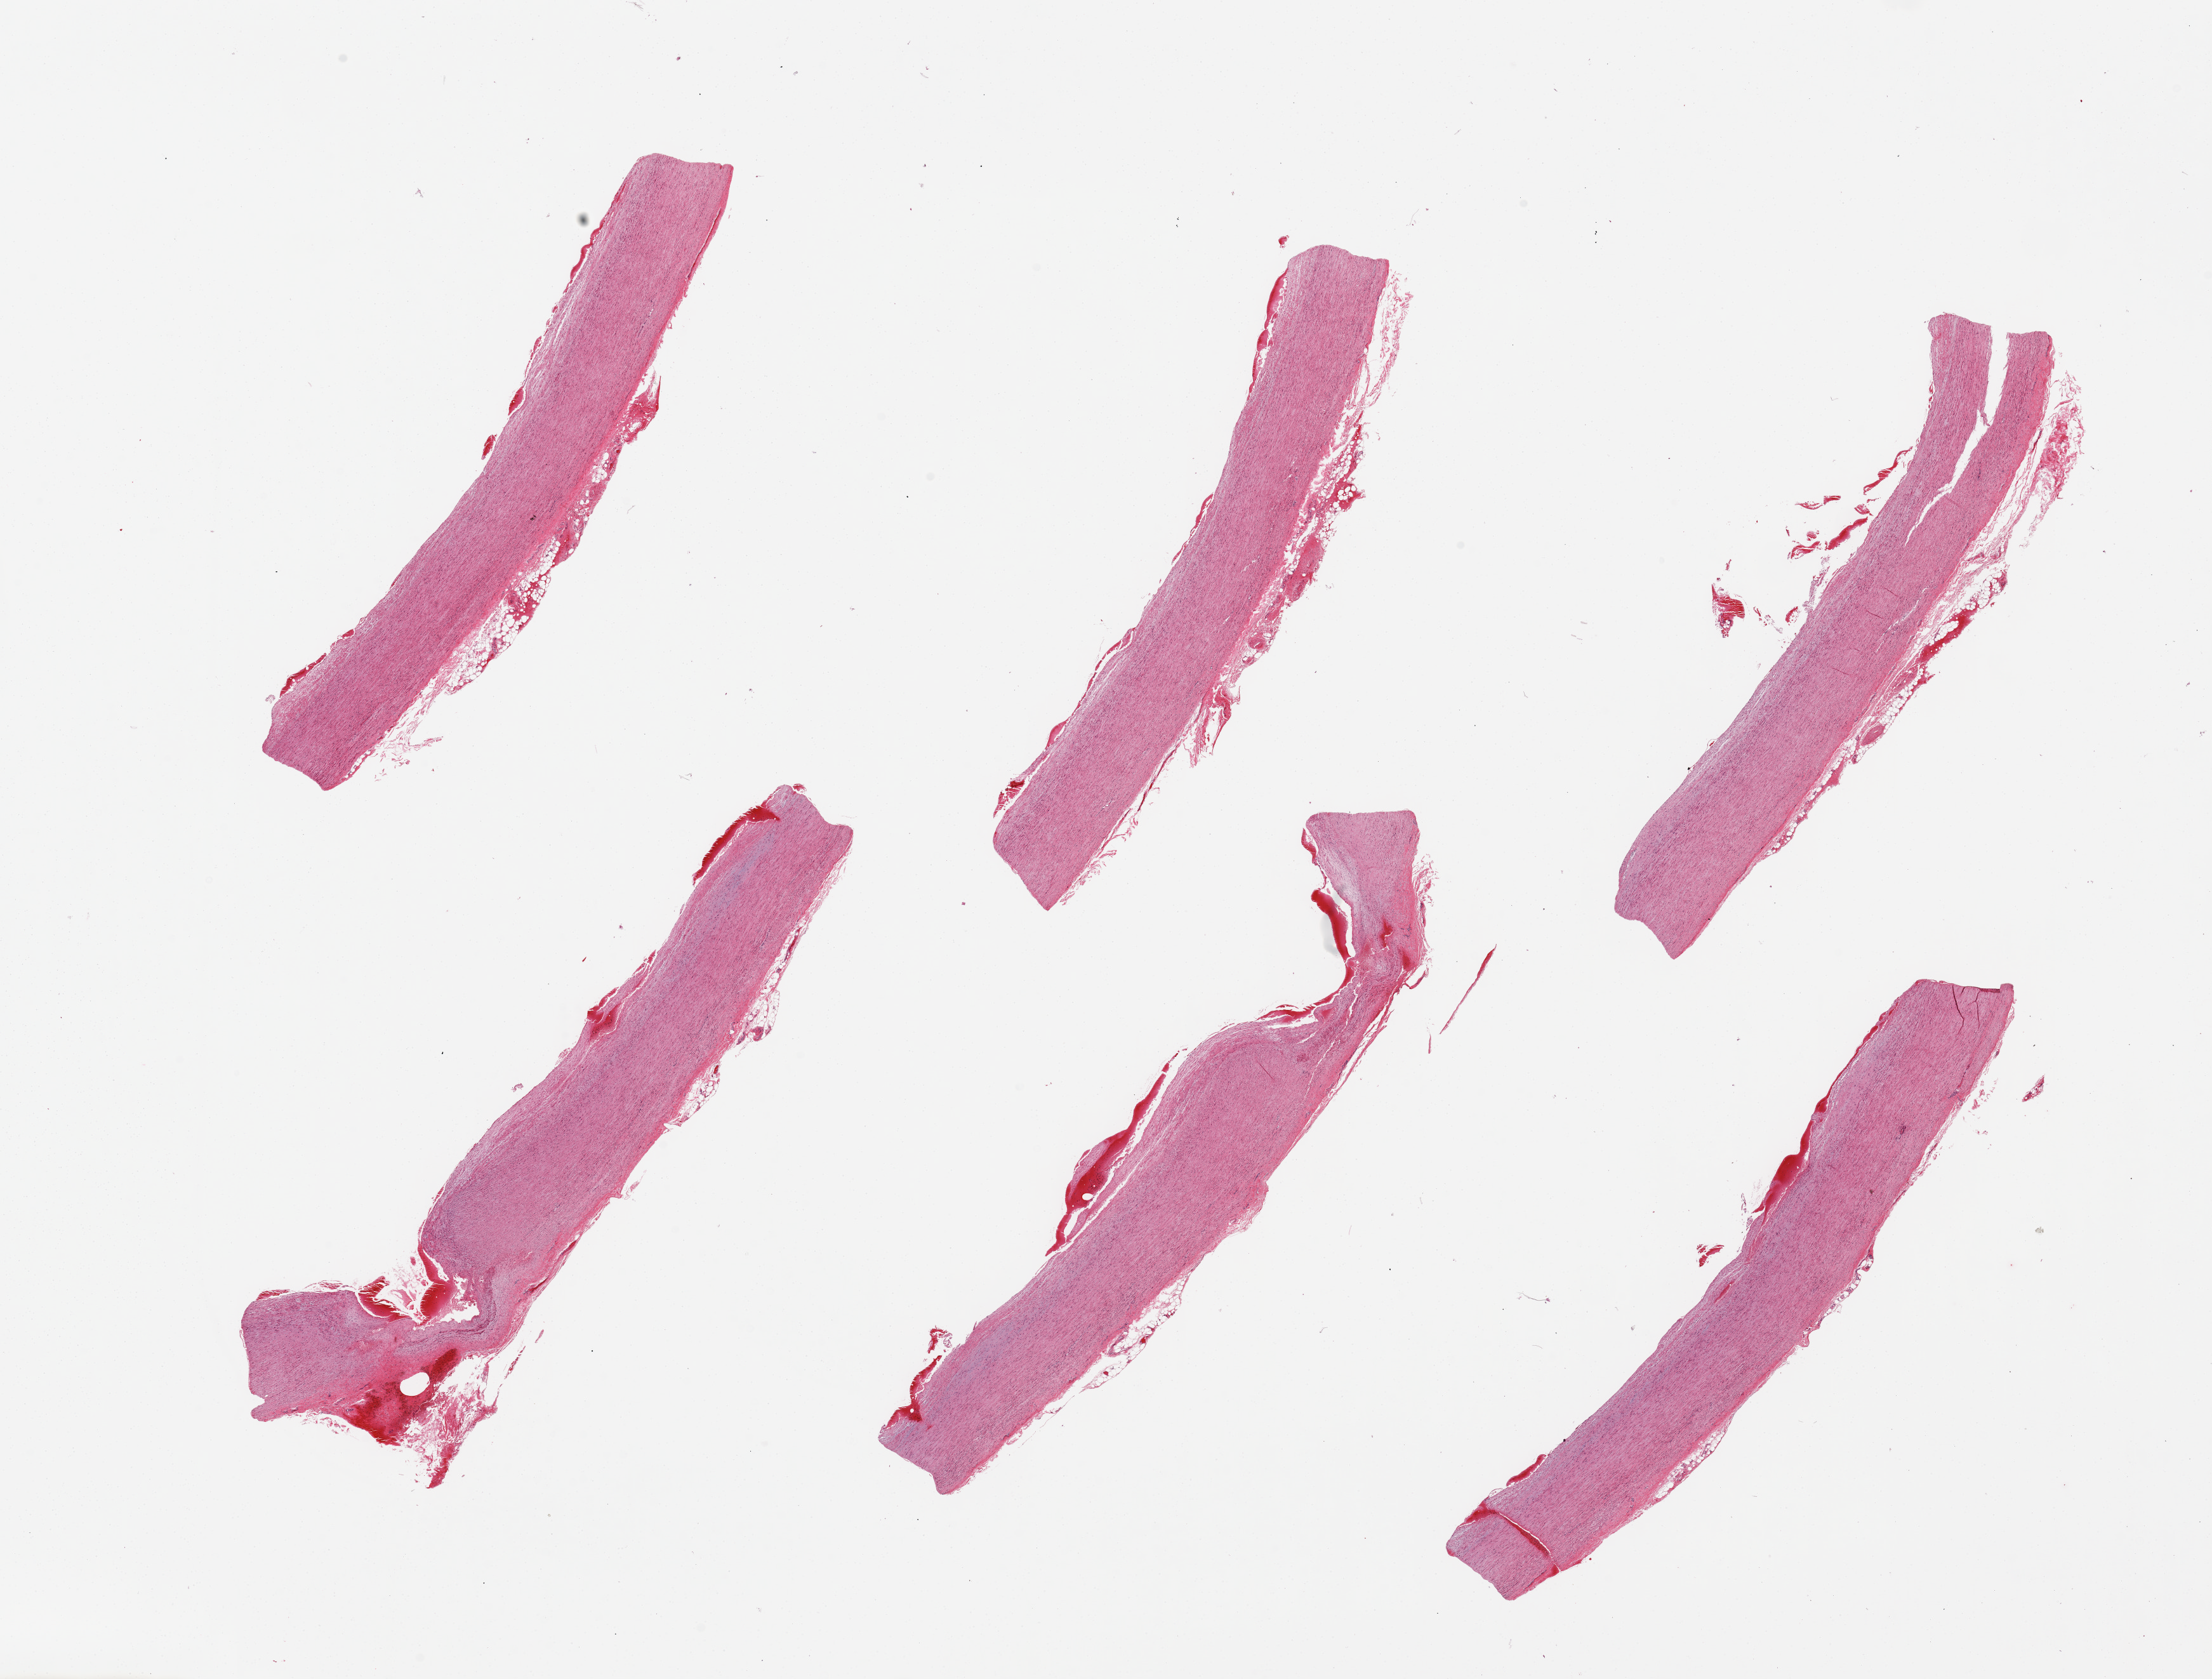
Digitized haematoxylin and eosin-stained section, brightfield, low-resolution overview of the scanned area, about 27.6 x 20.9 mm, PAXgene-fixed, paraffin-embedded tissue, target tissue: aorta, donor tissue sample. Donor: female.
Review note (as recorded): 6 pieces, some with adherent serosa ~0.5mm.